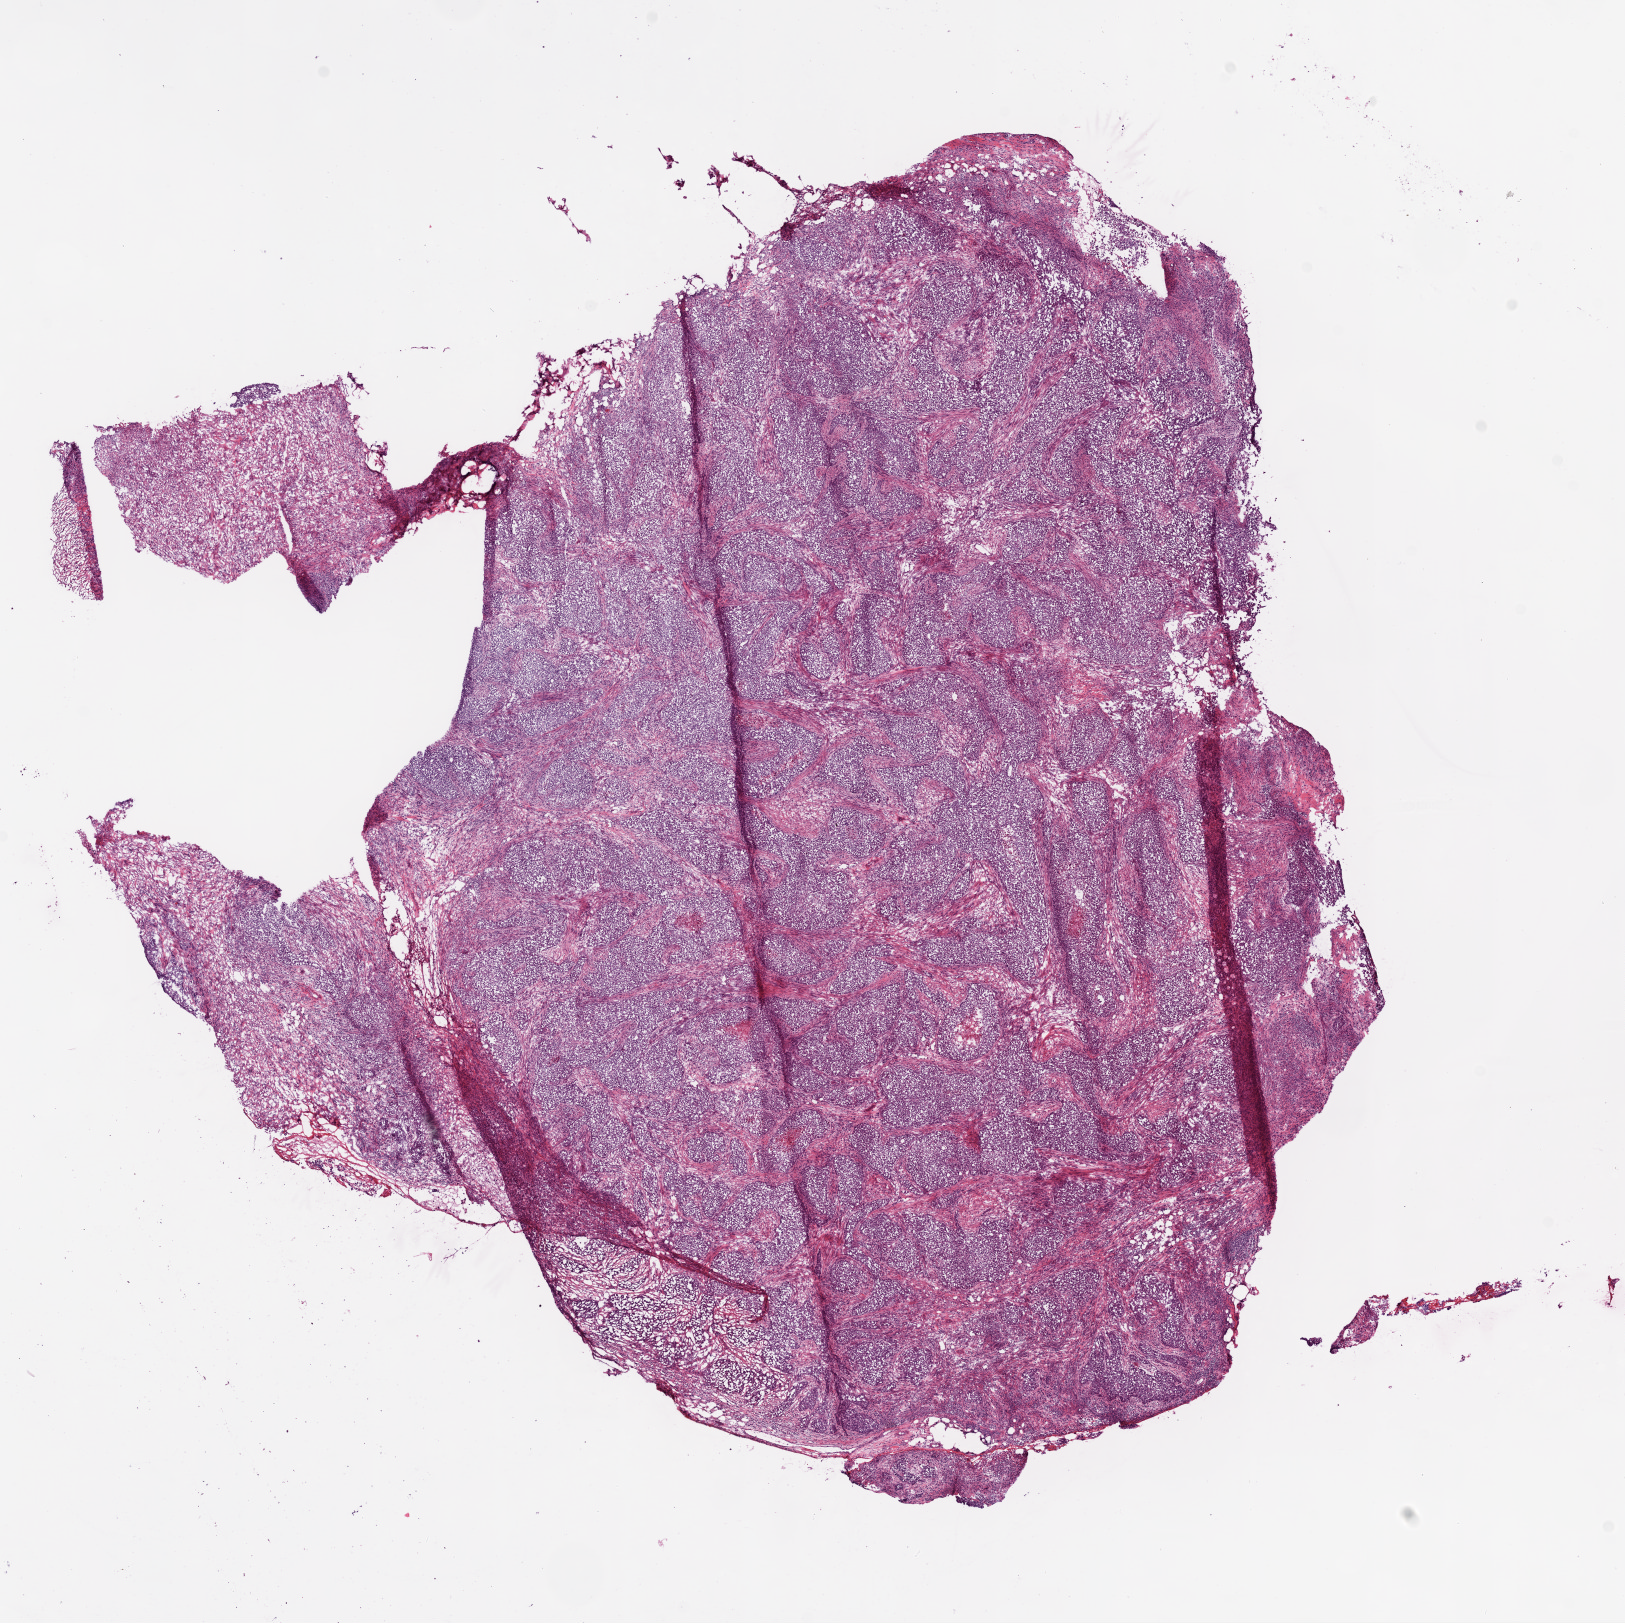
Whole-slide histology image, H&E, shown as a low-resolution overview of the whole scanned area (about 13.0 x 13.0 mm, slide scanned at 20x). Frozen section. Primary tumour sample from the ovary. Female patient; age at initial diagnosis 61 years. Histologic grade: G3 (poorly differentiated). Slide review estimates, as recorded: tumour cells 90%, tumour nuclei 90%, normal cells 0%, stromal cells 8%, necrosis 2%.
Laterality: bilateral. FIGO stage: IIIC. Diagnosis: Serous cystadenocarcinoma, NOS.